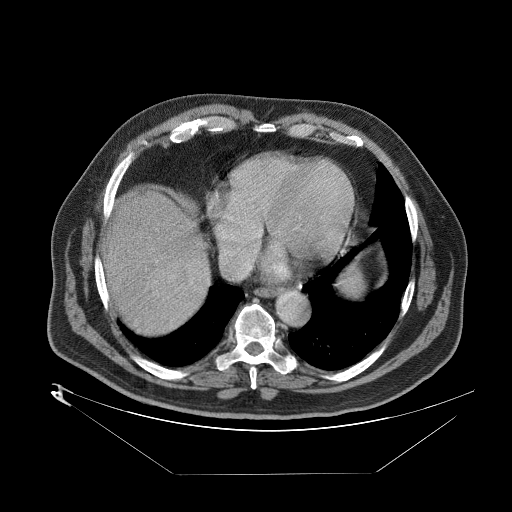
Contrast-enhanced abdominal CT (liver protocol), one axial slice. Slice 77 of 89 in the series (ordered by position). Reconstruction kernel STANDARD. 140 kVp. One of 2 acquisitions stored at this slice position. Soft-tissue window (W 400 / L 40 HU). 2.5 mm slice thickness. 512 × 512 image matrix. From the clinical record (not read from this slice): diagnosis: hepatocellular carcinoma (patient treated with transarterial chemoembolisation; whether this scan precedes or follows treatment is not stated here); TNM stage (as recorded): Stage-II; Child-Pugh class: B; tumour differentiation: moderately differentiated; tumour nodularity: multinodular.
Outlined on this slice (semi-automatic segmentation, software-assisted and operator-edited):
- abdominal aorta: bounding box [x1, y1, x2, y2] px = [275, 290, 310, 325]
- liver parenchyma outside the tumour (the mass and vessels are separate outlines, so this box may not span the whole liver): [102, 189, 206, 323]
- mass: [165, 265, 202, 301]
- liver vessels: [110, 274, 204, 304]